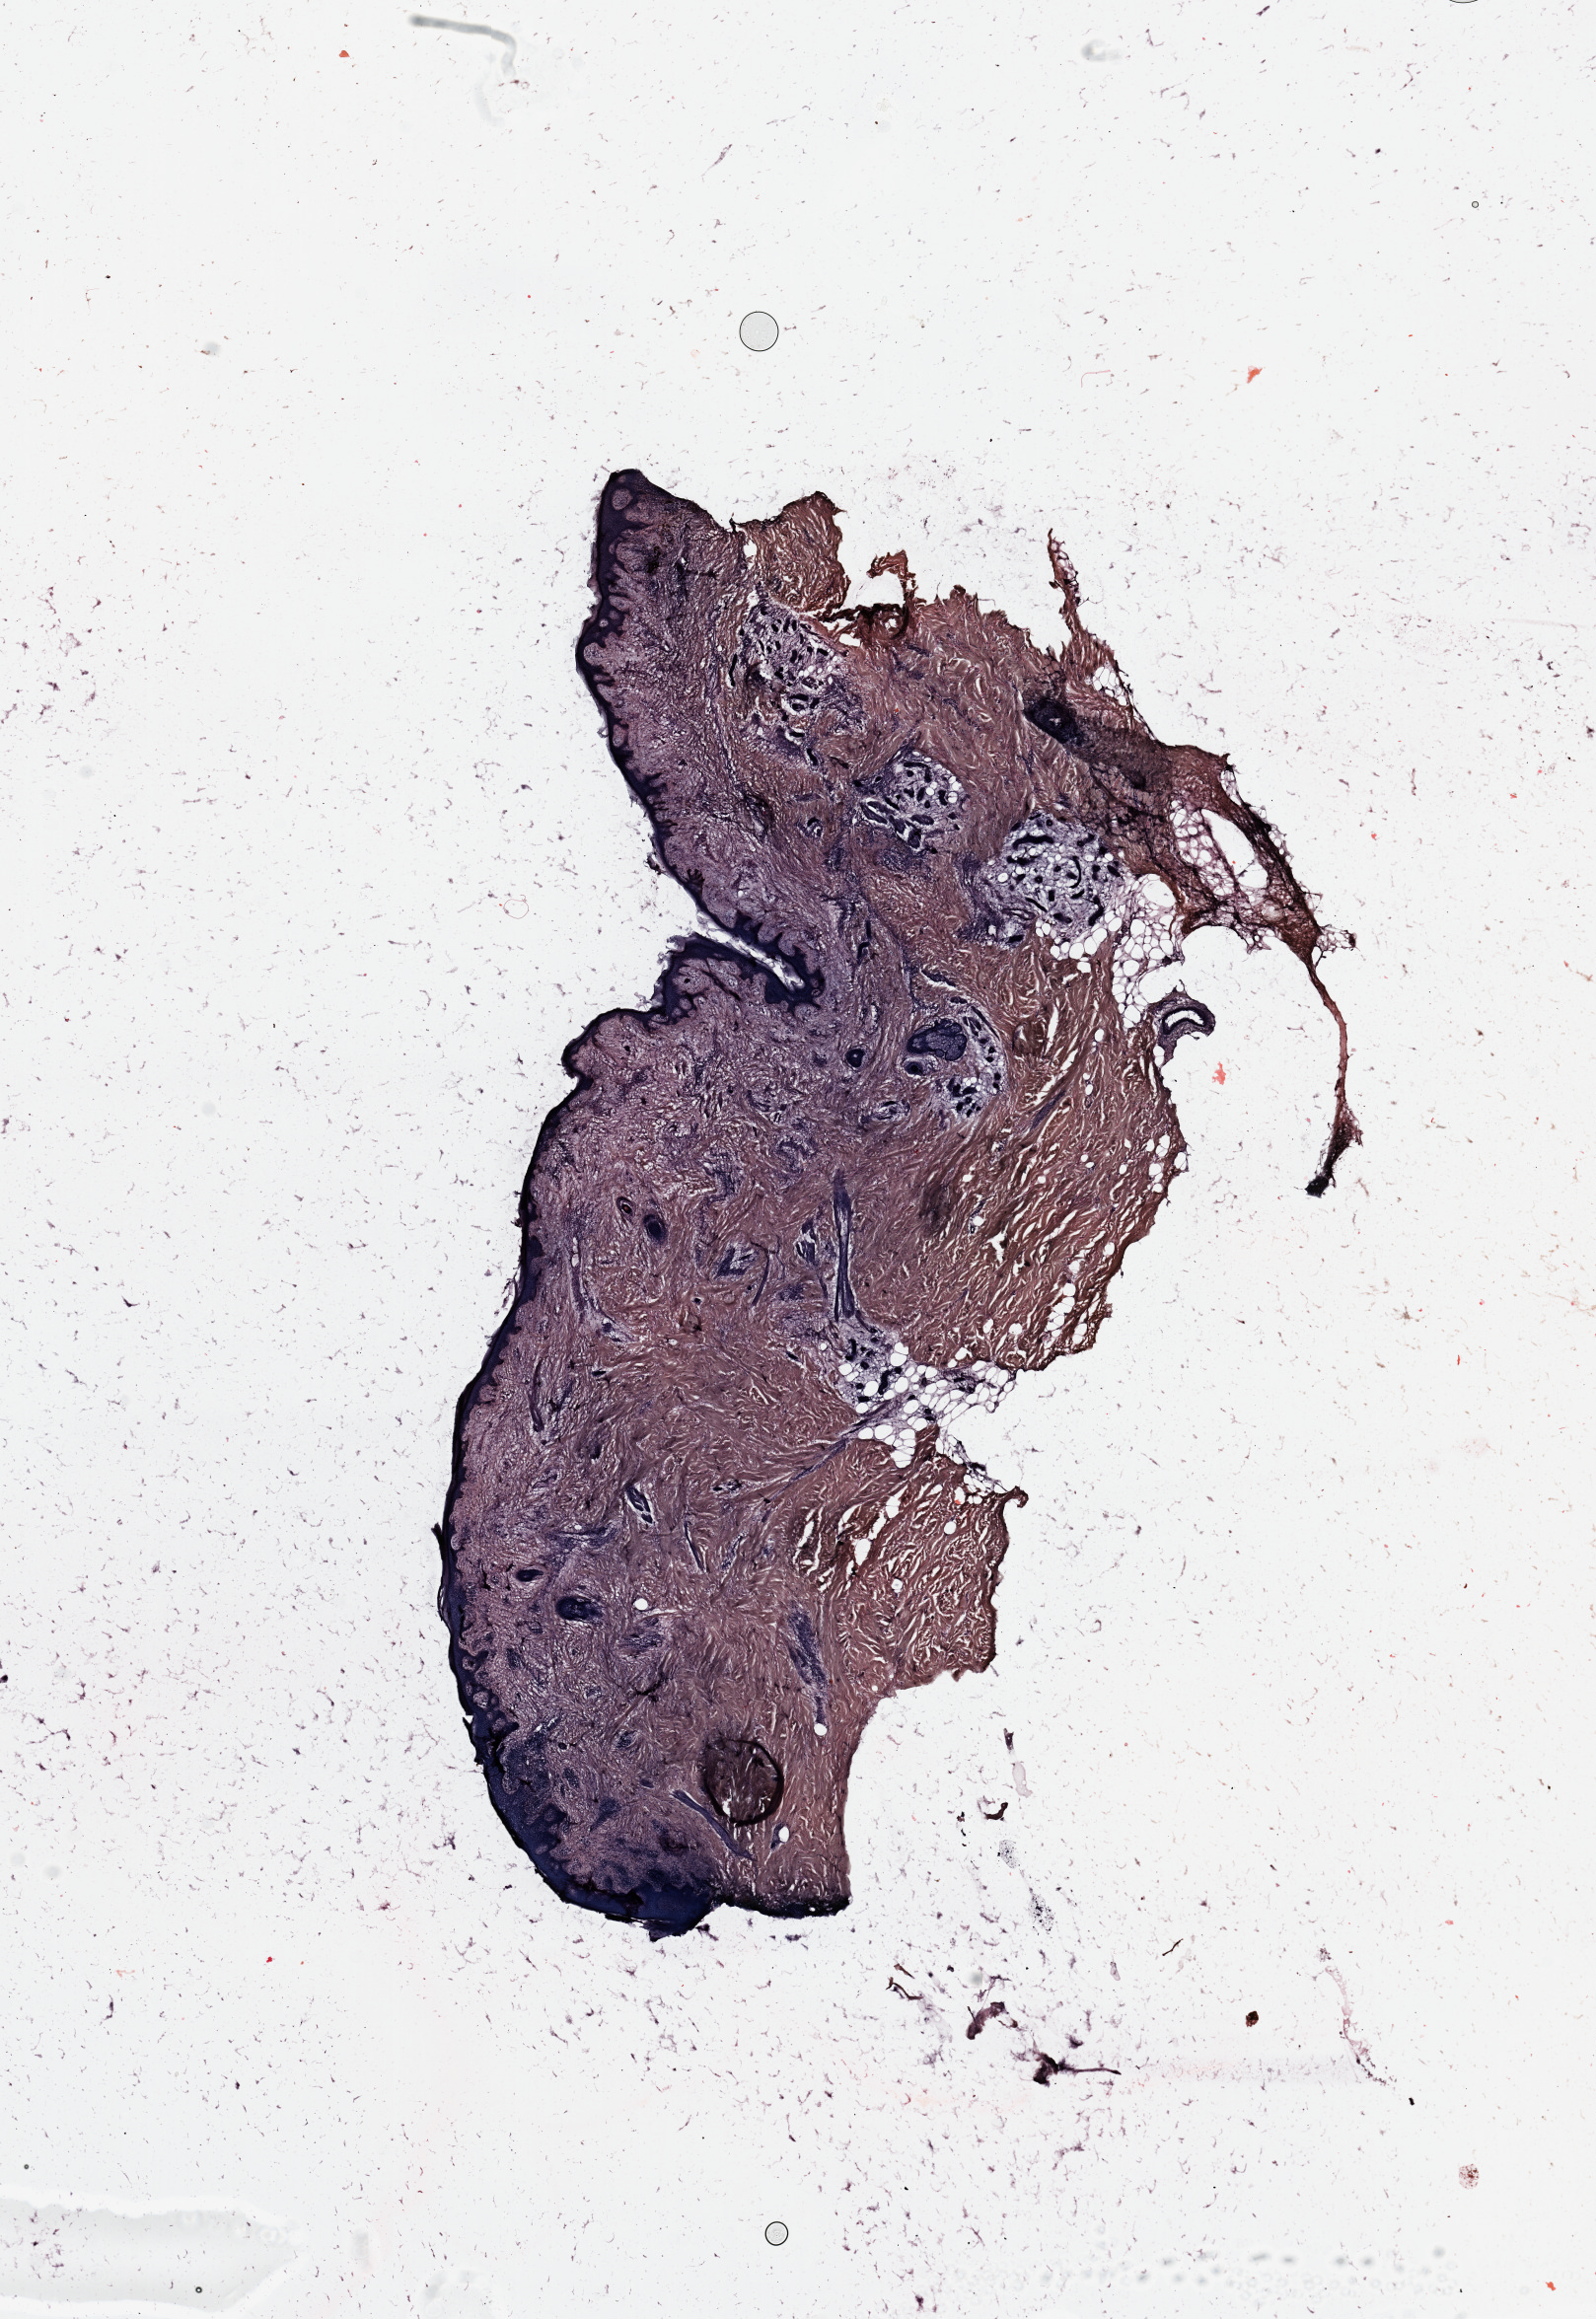
Digitized H&E-stained tissue section (whole slide) — shown as a low-resolution overview of the whole scanned area (about 12.8 x 18.6 mm, from a 20x scan). Normal (non-tumour) tissue (melanoma cohort); sampled site not recorded. Female, 67 y/o.
* this section: normal (non-tumour) tissue from the same patient
* patient diagnosis (cohort enrolment): cutaneous melanoma (skin)